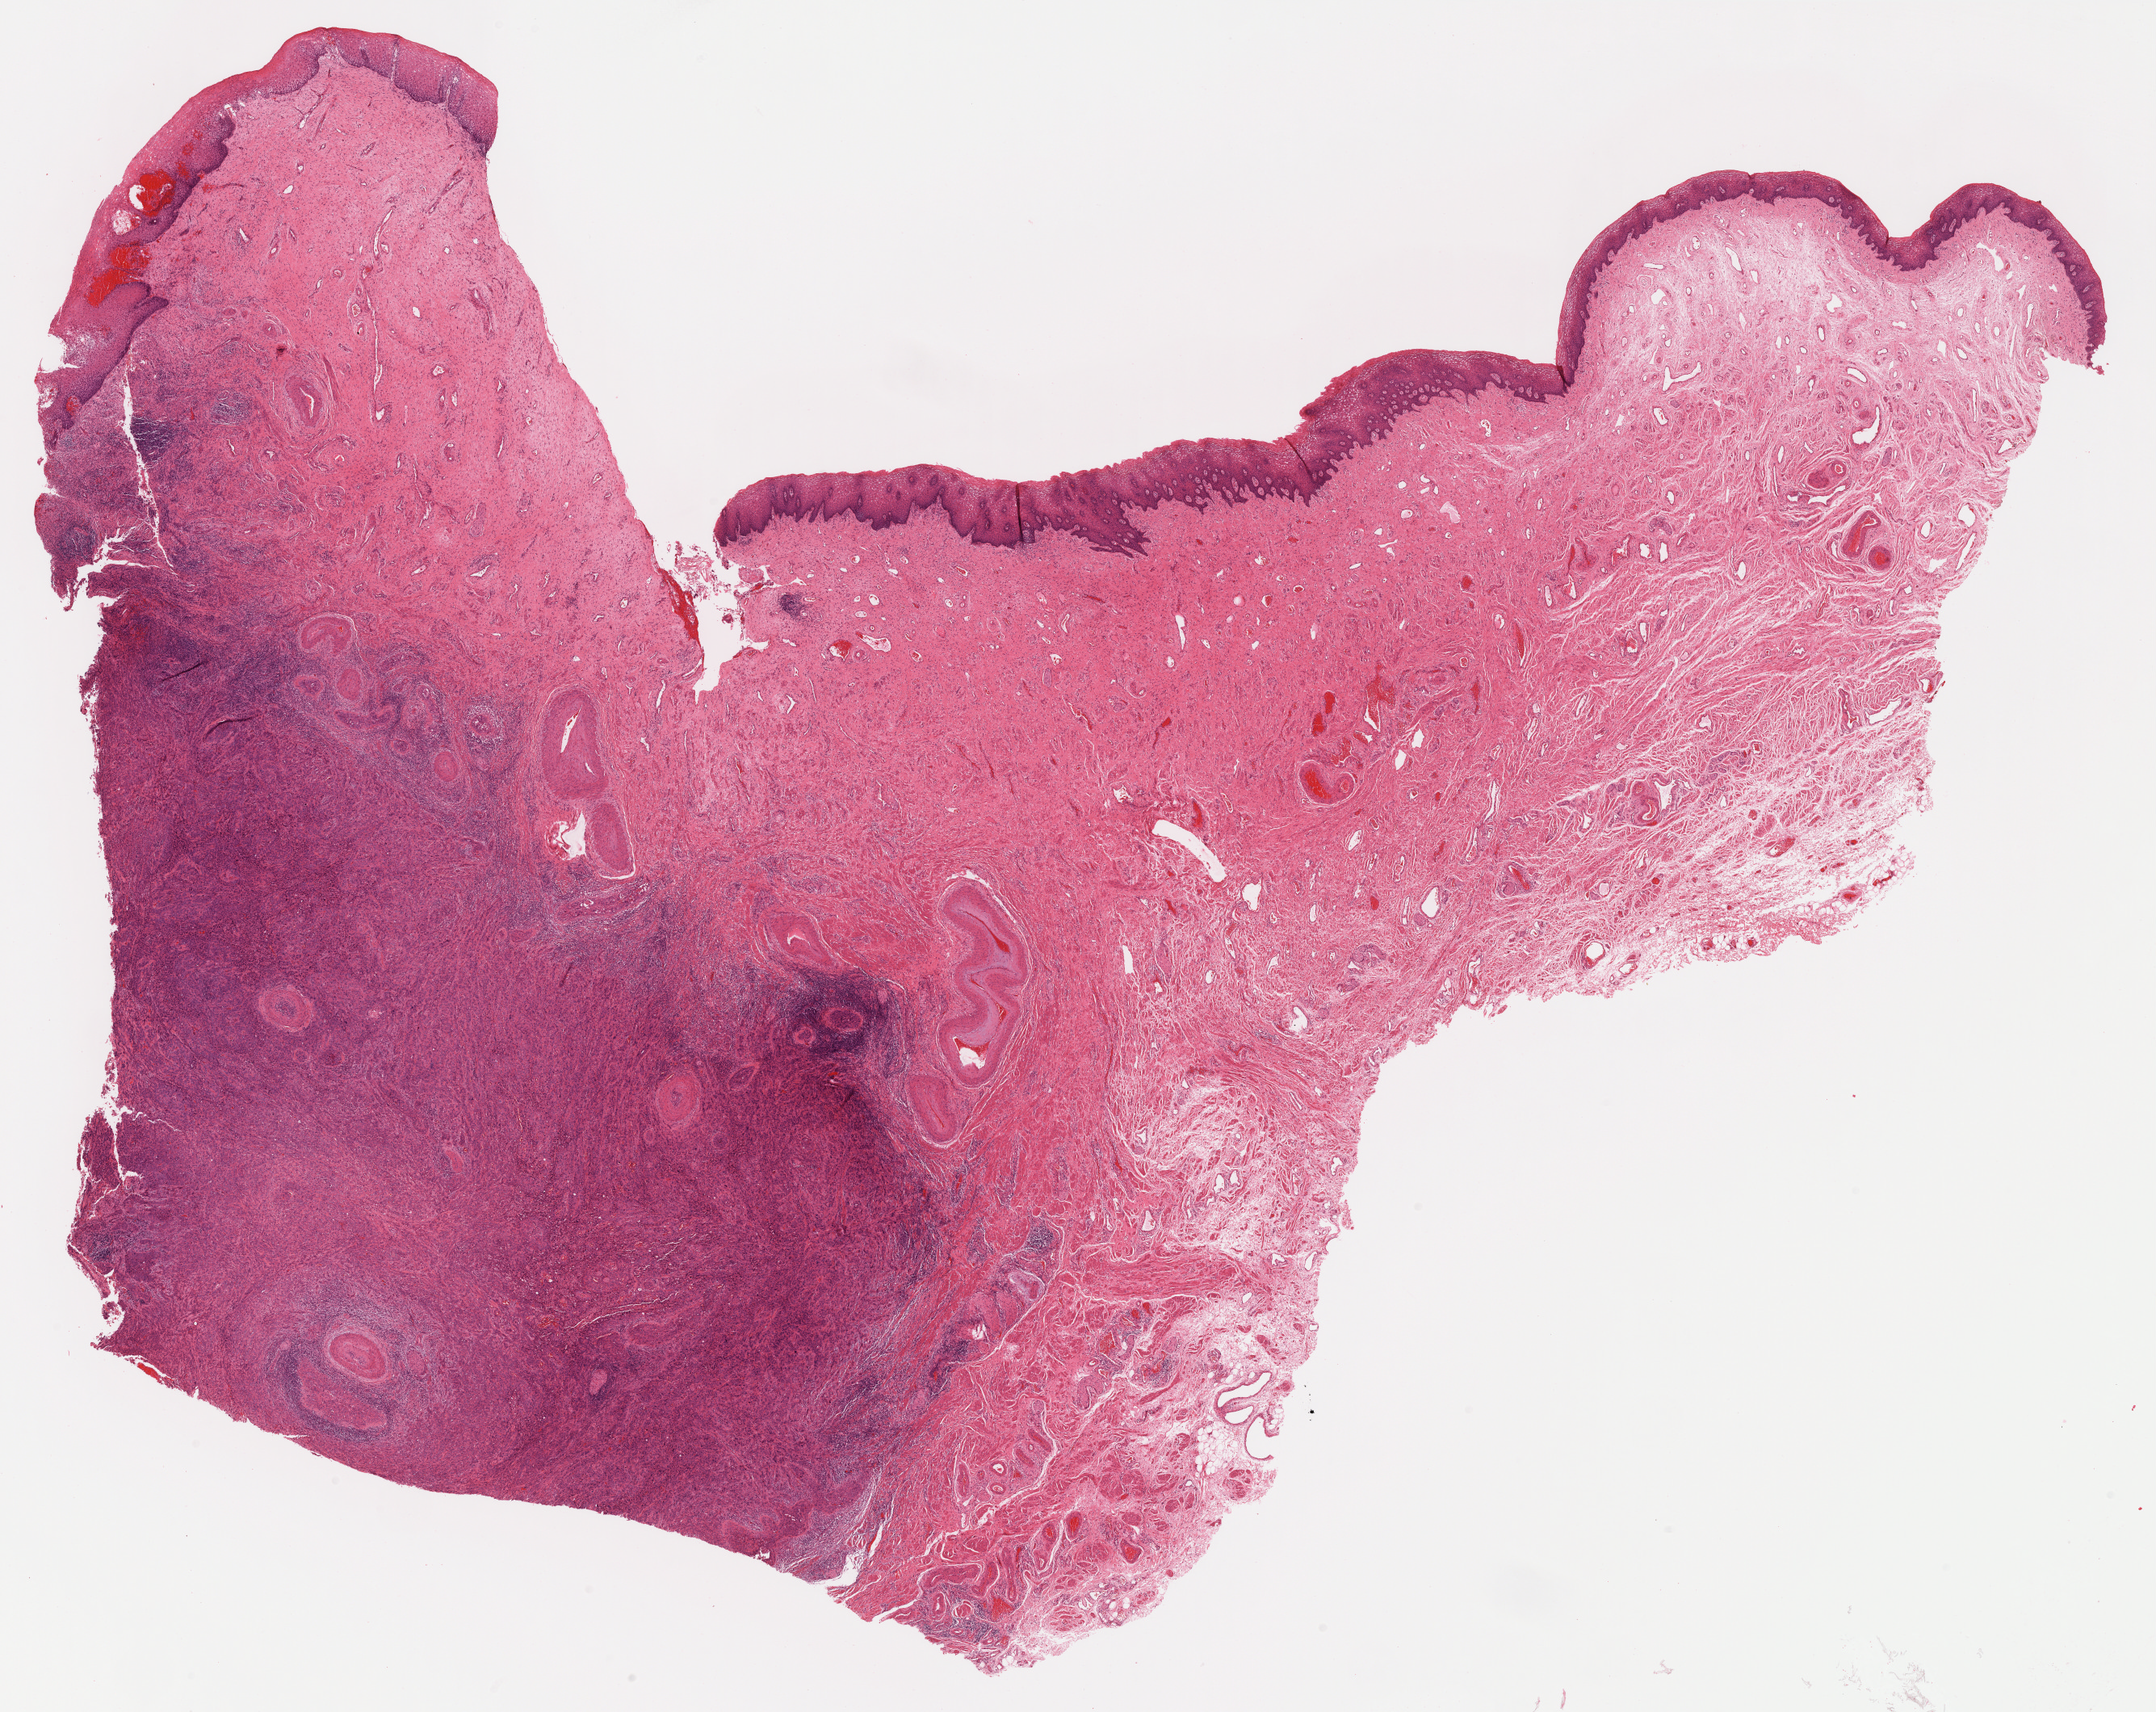
Digitized Hematoxylin and eosin (H&E) stained tissue section (whole slide) — low-resolution overview of the scanned area, about 21.4 x 17.0 mm (acquisition: 40x scan), FFPE section, primary tumour sample from the cervix. Patient: female, age at initial diagnosis 38 years. Histologic grade: G3 (poorly differentiated).
• histologic diagnosis: Squamous cell carcinoma, keratinizing, NOS (cervix uteri)
• FIGO stage: IB